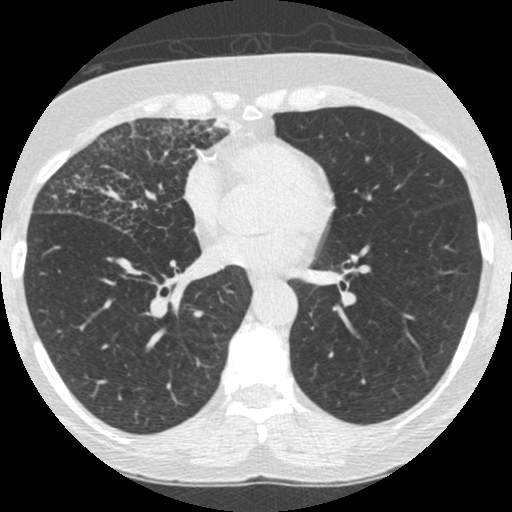
Low-dose screening chest CT, one axial slice. Slice 121 of 253 in the series (ordered by position). Reconstruction kernel STANDARD. 120 kVp. Lung window (W 1500 / L -600 HU). 1.25 mm slice thickness. 512 × 512 image matrix.
Annotated regions visible in this slice (outlined manually by an expert reader):
- lesion 4 (tumor, upper lobe of right lung): box from (x=186, y=115) to (x=240, y=153) px